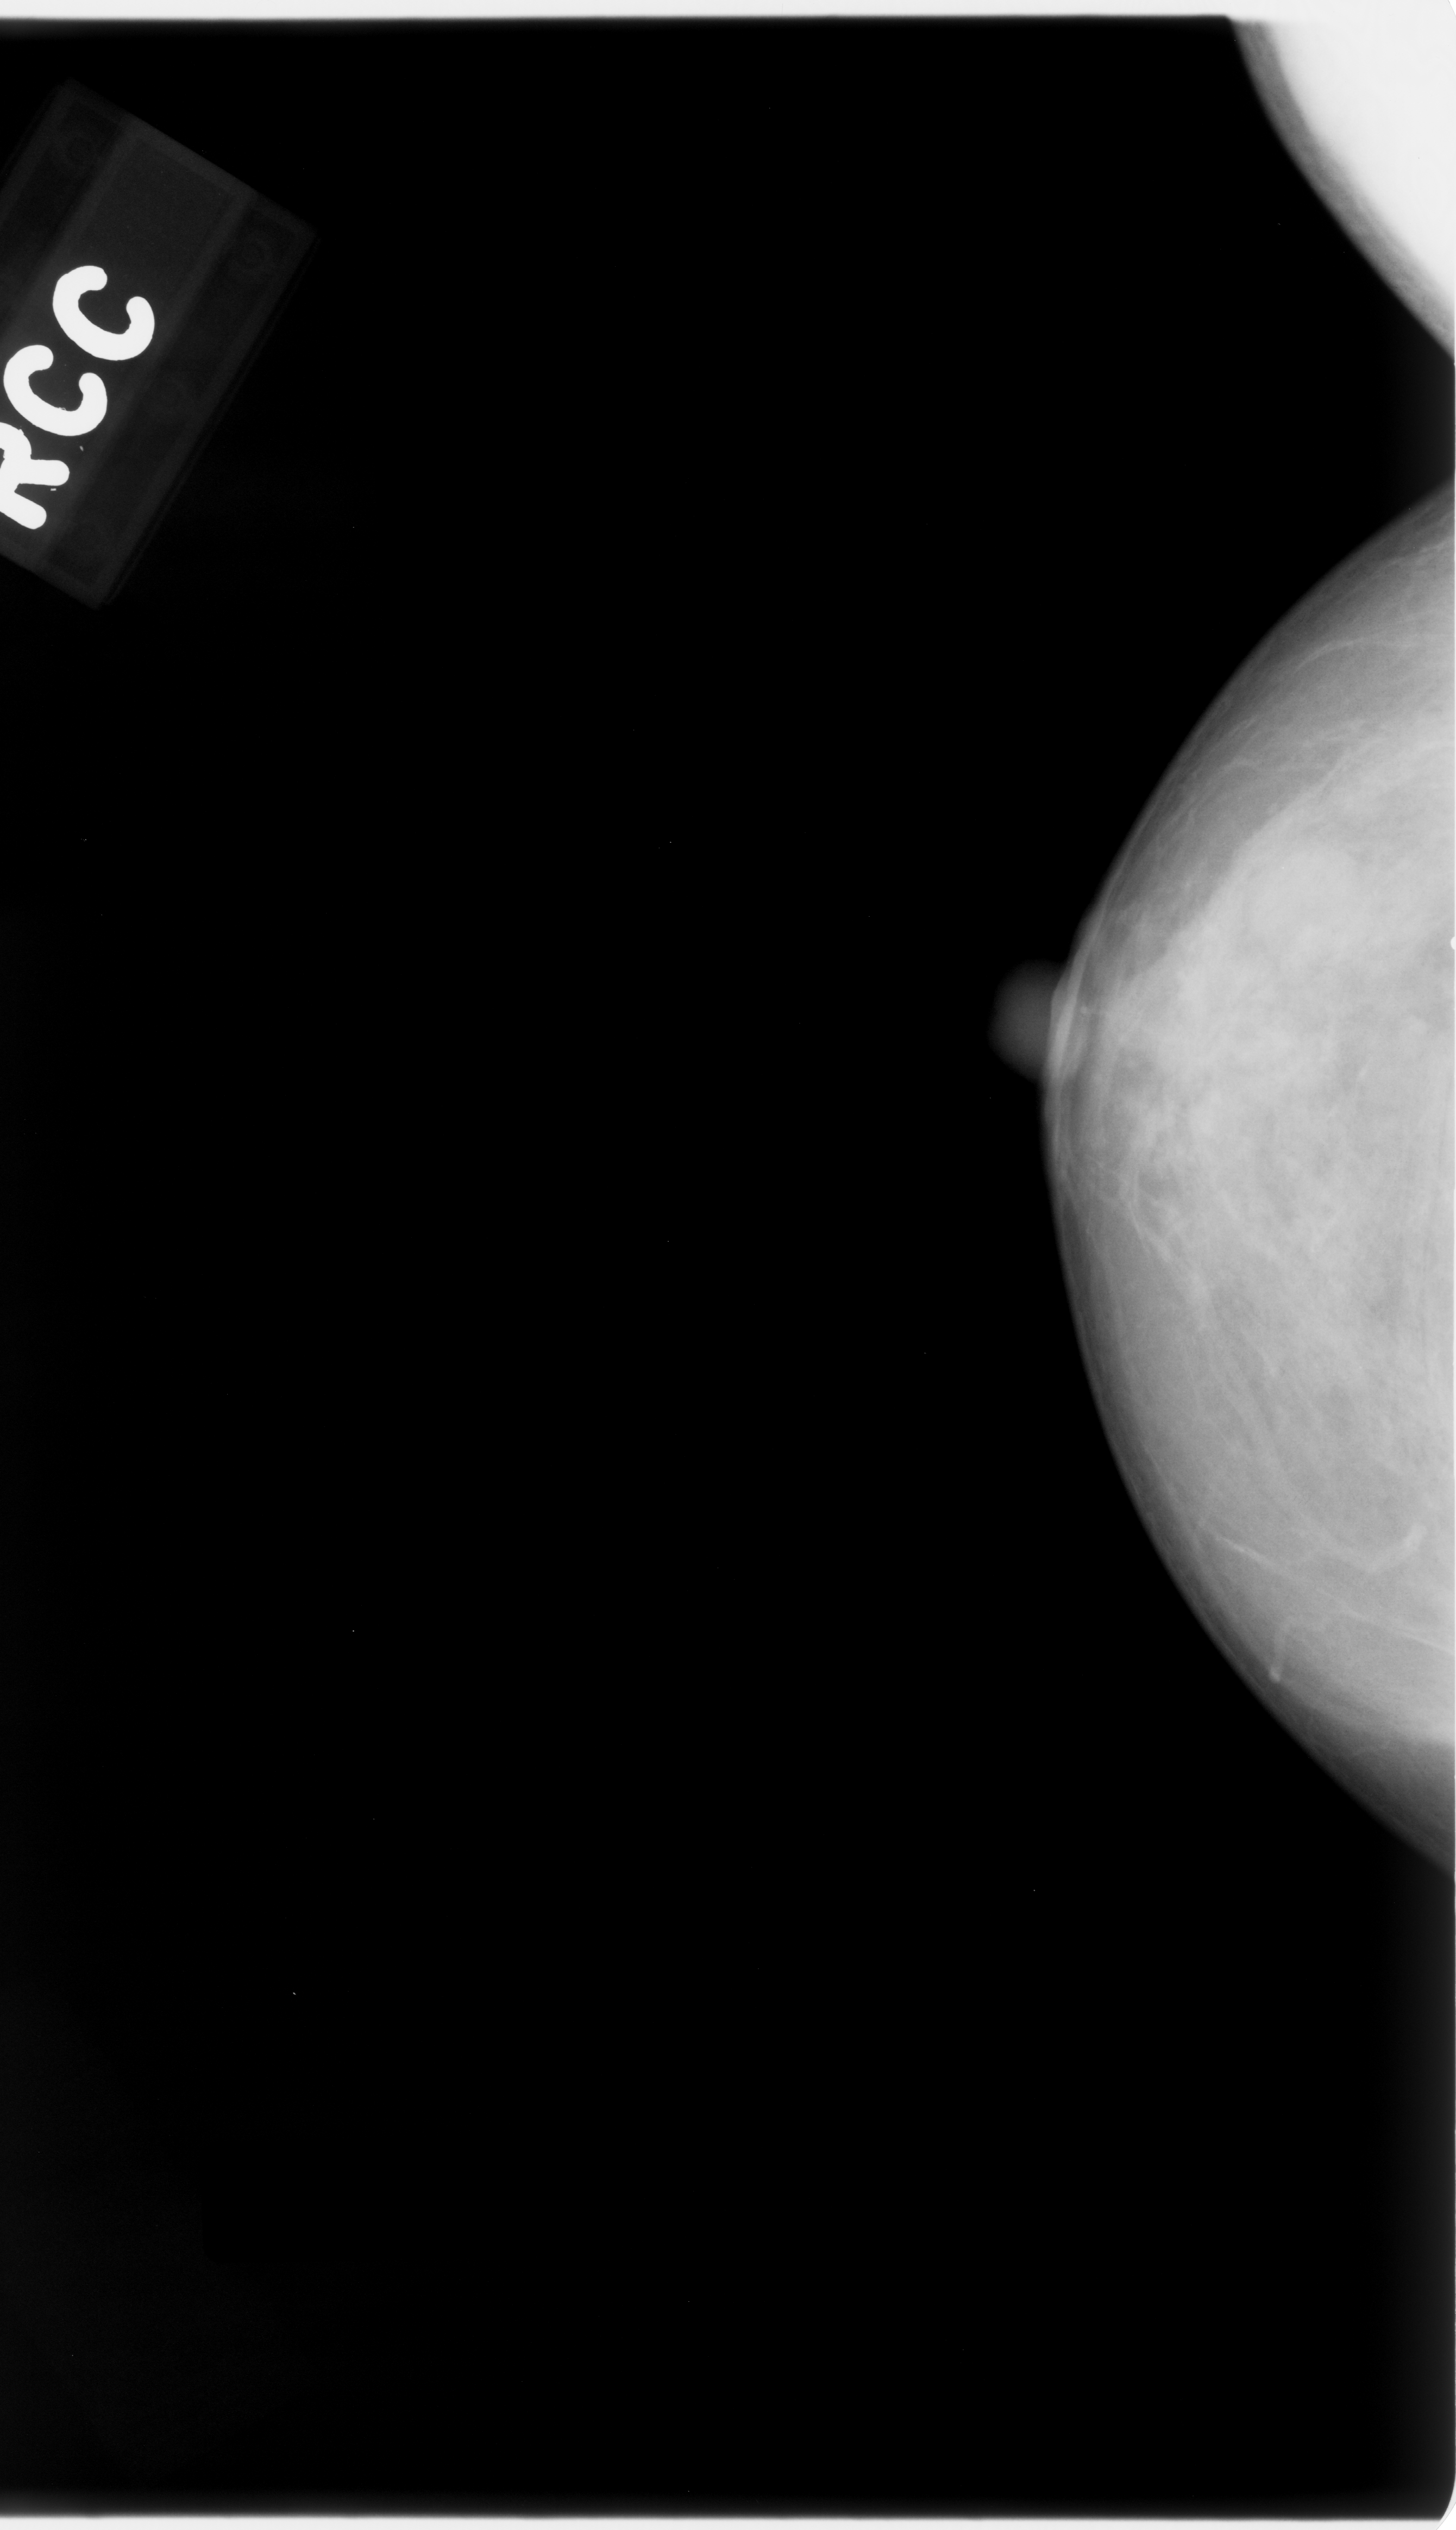
Digitized screen-film mammogram. Right breast. Craniocaudal (CC) view. BI-RADS breast density category 3 (scale 1–4). 1456 × 2530 image matrix.
Marked abnormalities (boxes around the expert regions of interest):
- mass, shape oval, margins microlobulated; BI-RADS assessment category 4; subtlety rating 4 on a 1 (subtle) to 5 (obvious) scale; pathology (as recorded): benign: bounding box [x1, y1, x2, y2] px = [1256, 835, 1358, 978]